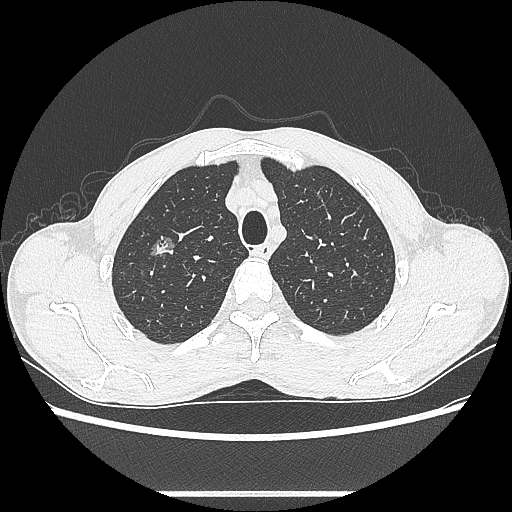
Chest CT, one axial slice; reconstruction kernel LUNG; 100 kVp; lung window (W 1500 / L -600 HU); 512 × 512 image matrix, field of view 357 × 357 mm. Patient: male, 54 years. Case-level facts recorded for this patient, not image findings: clinical TNM (as recorded): T1a N0 M0.
Structures marked on this image (rectangle marked by the reading radiologist):
- lung tumour (recorded histology: adenocarcinoma): box from (x=142, y=230) to (x=183, y=264) px